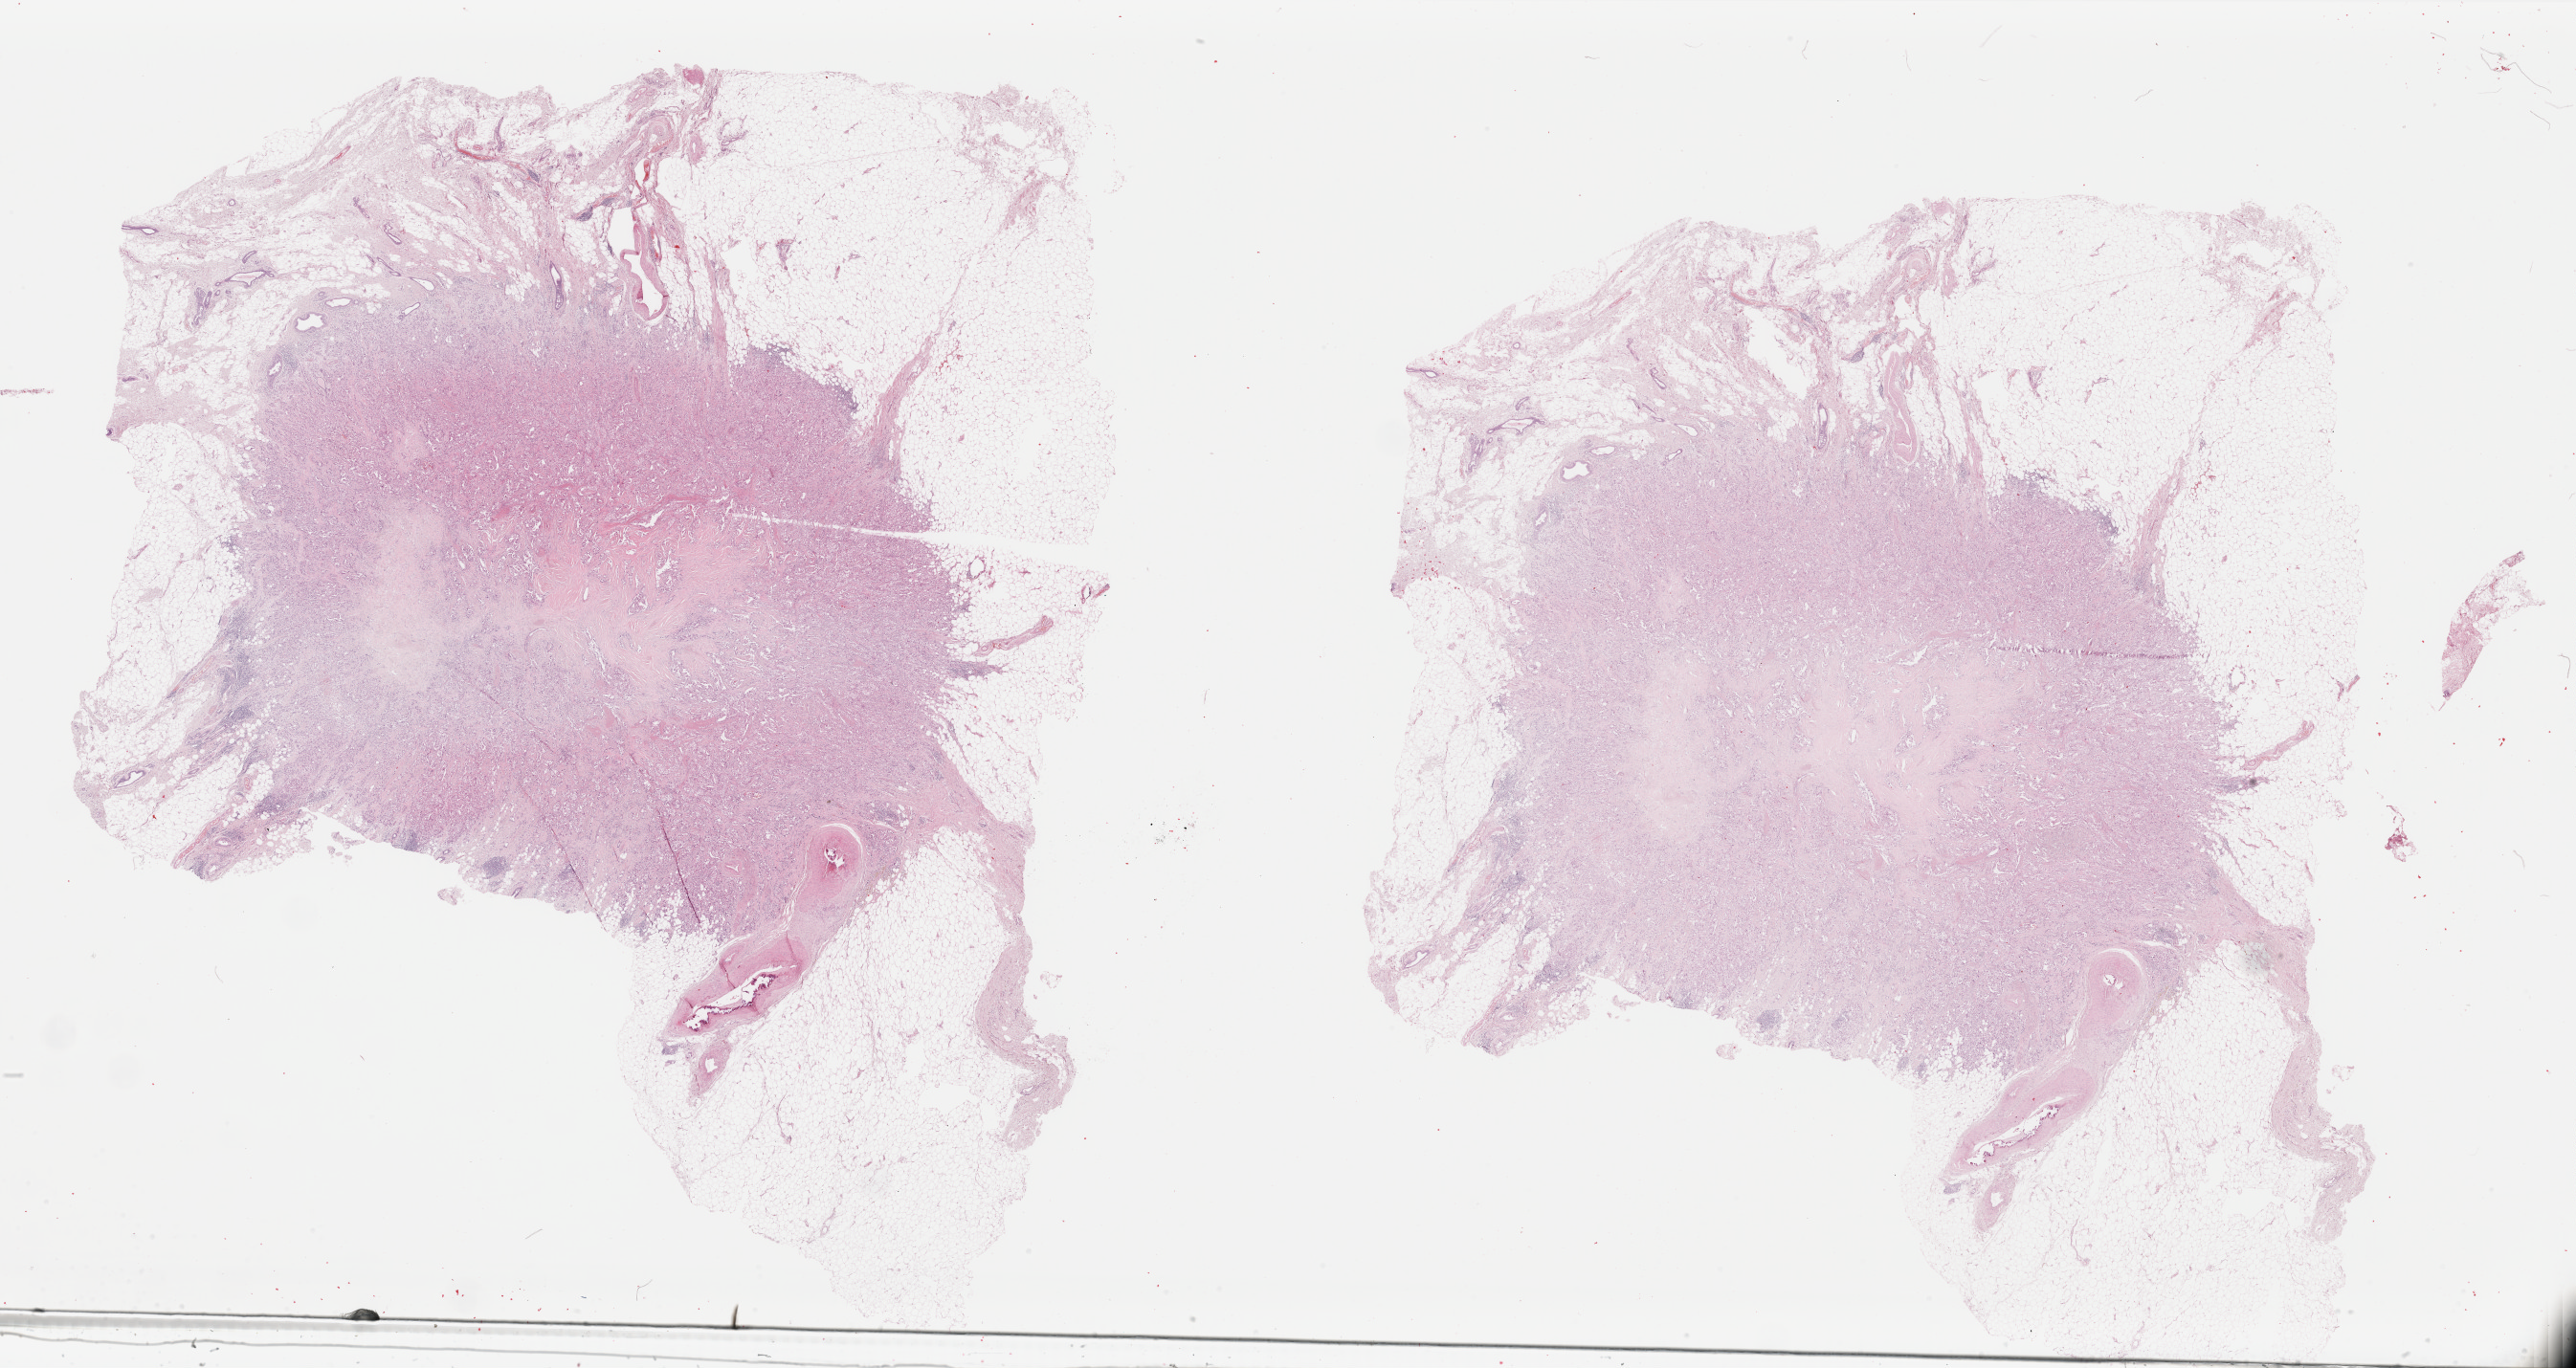
Whole-slide histology image, H&E-stained, shown as a low-resolution overview of the whole scanned area (about 42.7 x 22.7 mm, acquisition: 40x scan); FFPE section; breast, primary tumour sample. Patient: female, age at initial diagnosis 79 years.
- TNM: T1c N2a M0
- histologic diagnosis: Infiltrating duct carcinoma, NOS
- AJCC pathologic stage: IIIA (7th edition)
- lymph nodes positive (case pathology): 8 of 25 examined